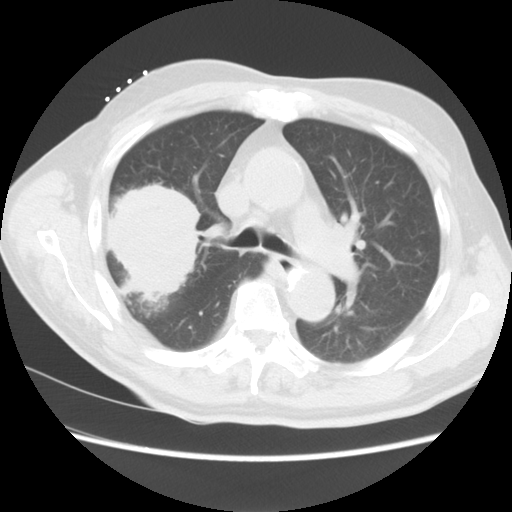
Chest CT, one axial slice; position 9 of 15 along the scan axis; reconstruction kernel STANDARD; lung window (W 1500 / L -600 HU); 512 × 512 image matrix, field of view 350 × 350 mm. Male patient, age 68 years. From the clinical record (not read from this slice): clinical TNM (as recorded): T4 N3 M0.
Outlined on this slice (rectangle marked by the reading radiologist):
- lung tumour (recorded histology: squamous cell carcinoma): bounding box (x1, y1, x2, y2) in pixels: (112, 174, 209, 301)